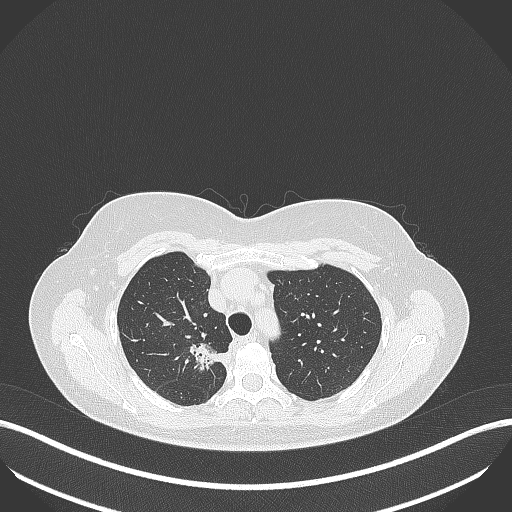
Chest CT, one axial slice. Slice 301 of 386 in the series (ordered by position). Lung window (W 1500 / L -600 HU). 512 × 512 image matrix, field of view 400 × 400 mm. Patient: female, 65 years. Case-level facts recorded for this patient, not image findings: clinical TNM (as recorded): T1b N0 M0; histopathological grade: G2.
Annotated regions visible in this slice (rectangle marked by the reading radiologist):
- lung tumour (recorded histology: adenocarcinoma): box from (x=185, y=336) to (x=230, y=372) px